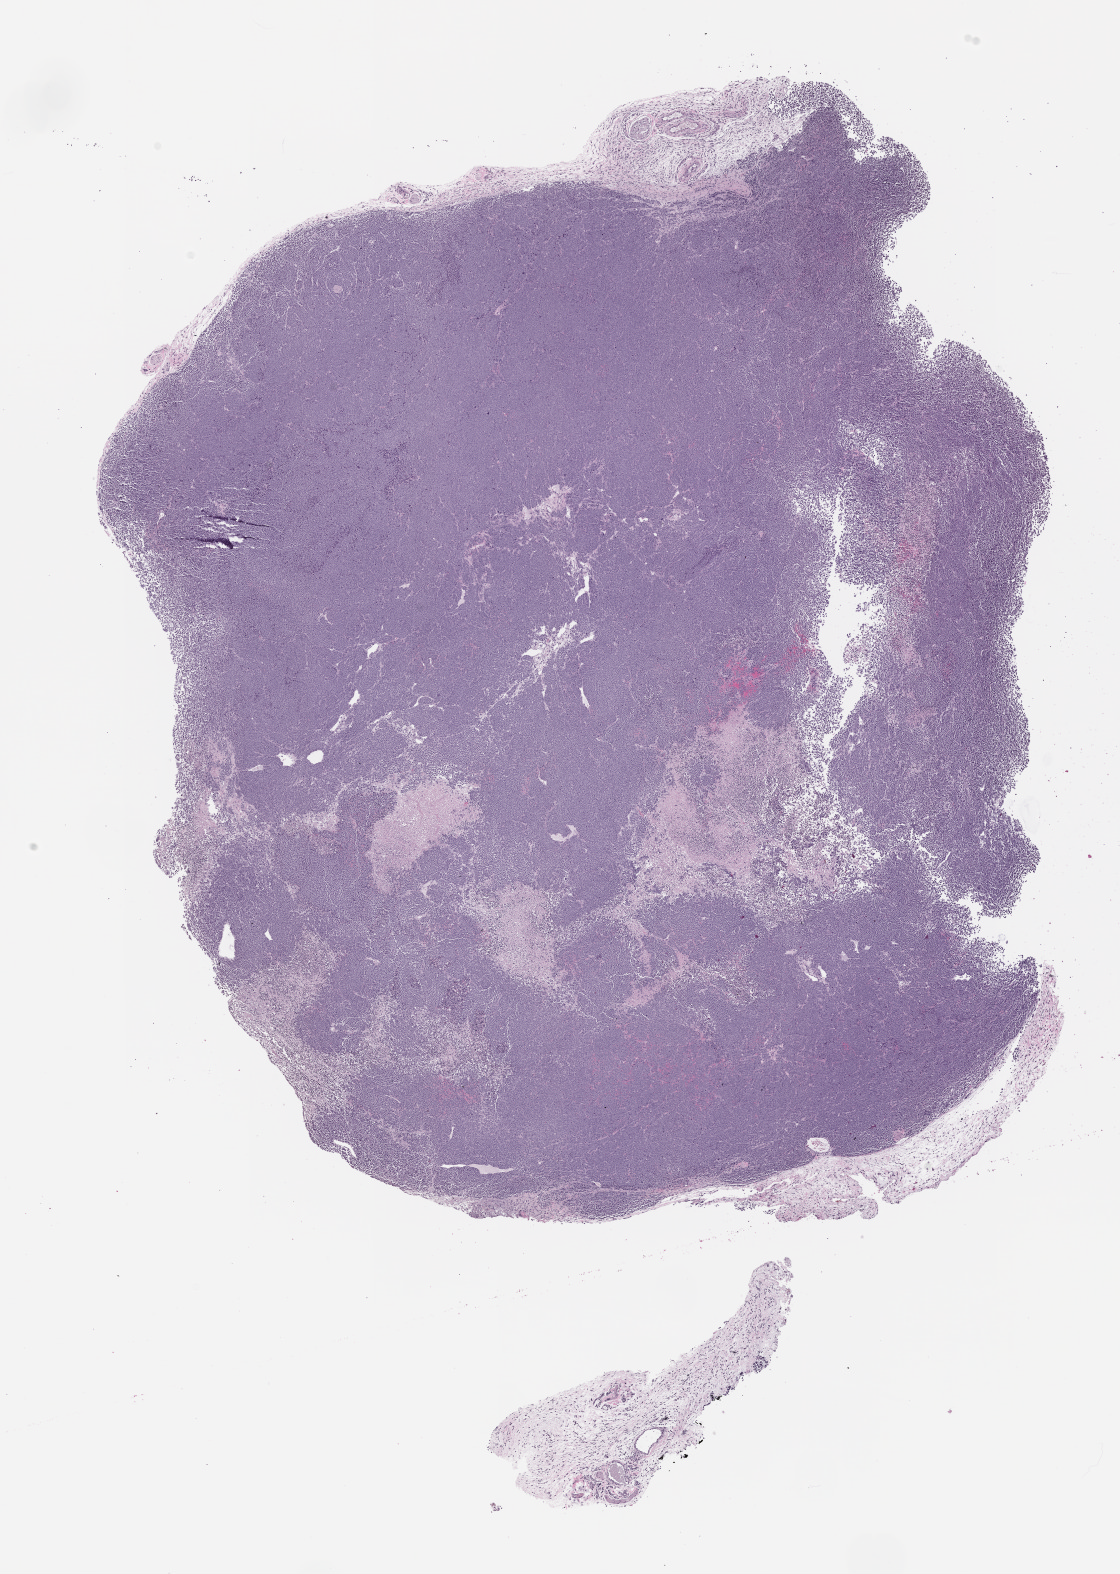
Whole-slide image, hematoxylin and eosin (H&E): patient-derived xenograft (human tumor grown in a mouse), passage 1 — a low-resolution overview of the entire scanned area, about 9.0 x 12.7 mm, formalin-fixed, paraffin-embedded (FFPE) tissue, originating tumor site category: endocrine.
Originating patient diagnosis: Merkel Cell Carcinoma.